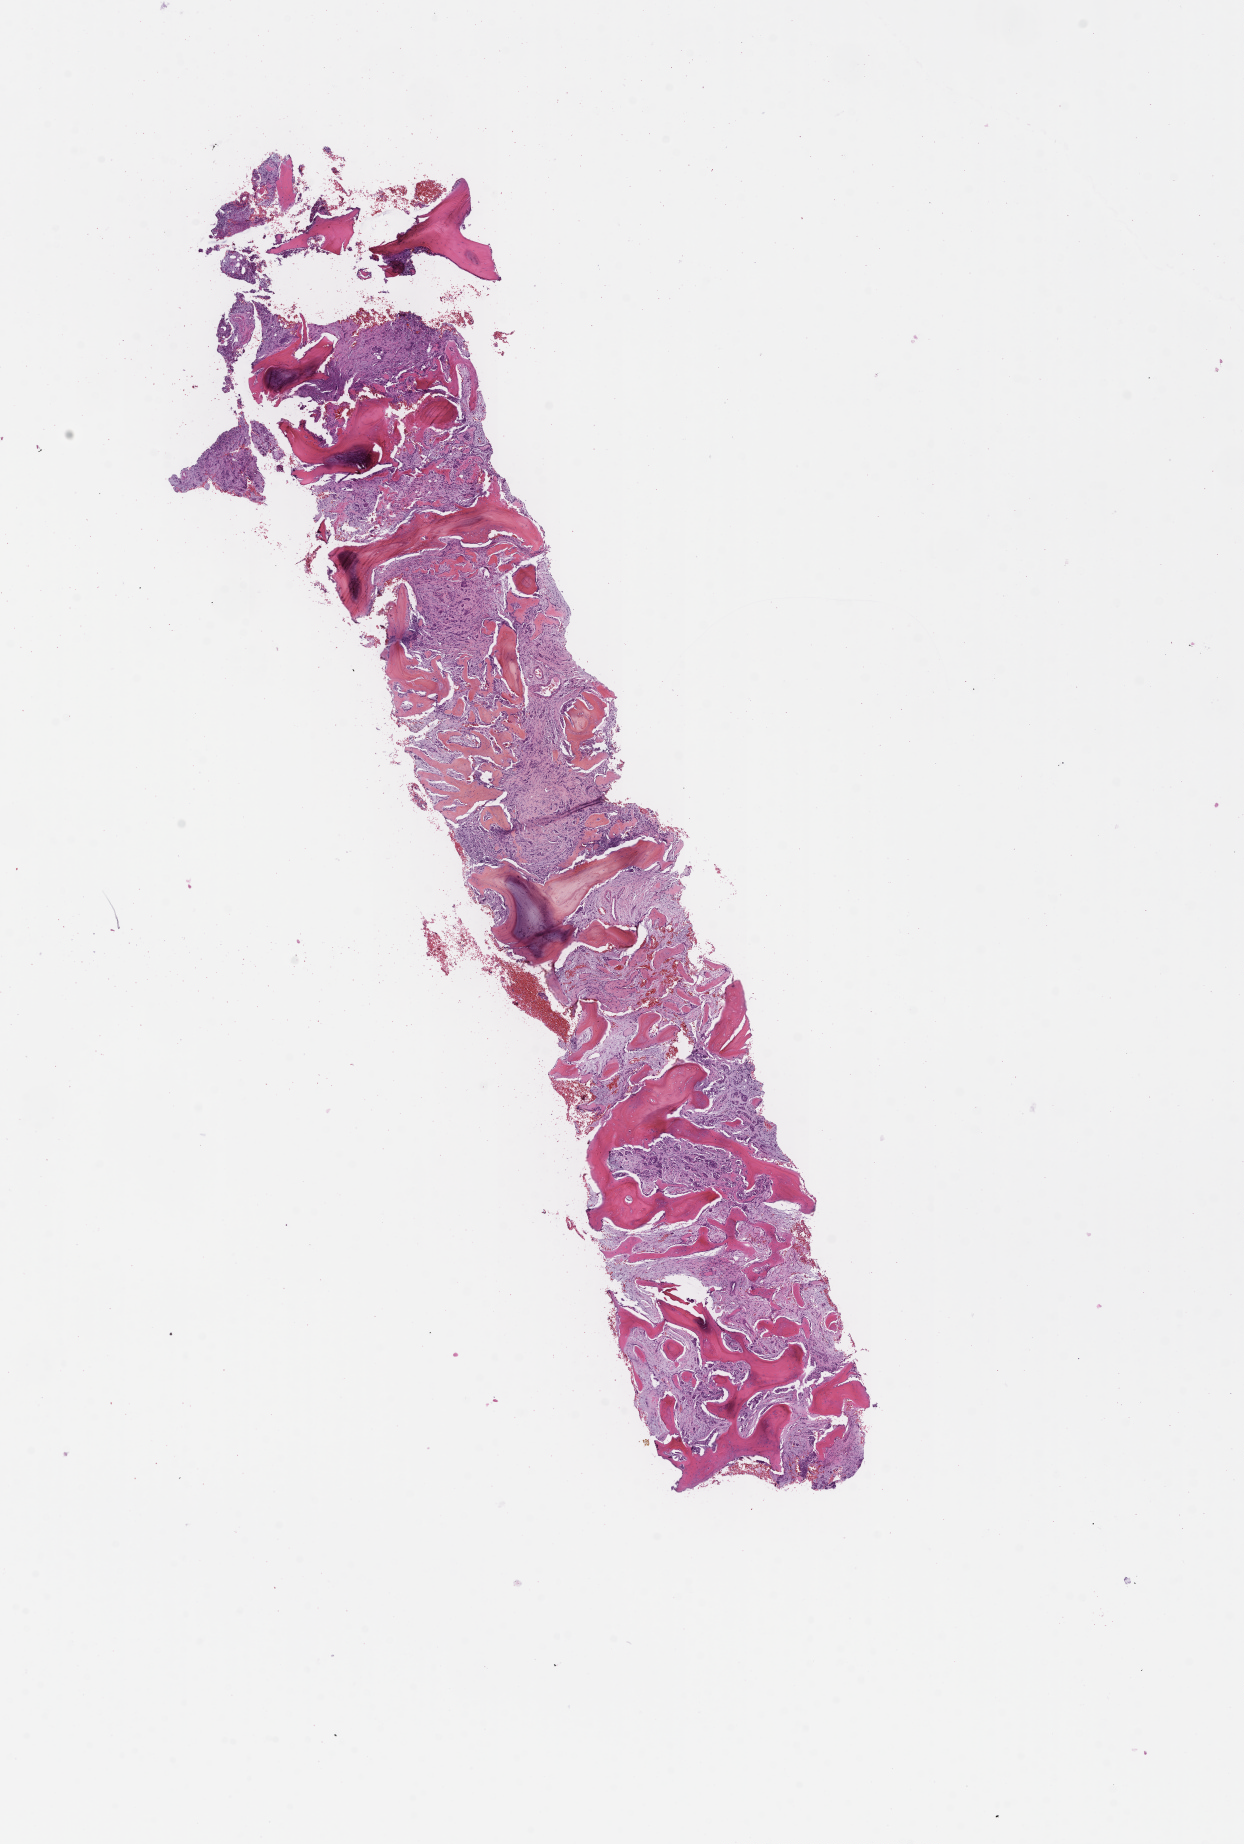
Digitized H&E-stained section, whole scanned area (about 10.1 x 14.9 mm) shown as a low-resolution overview. FFPE section. Specimen time point: collected at baseline (before treatment). Female patient.
• this section: metastatic tumor tissue
• primary diagnosis of the patient: Invasive Breast Carcinoma